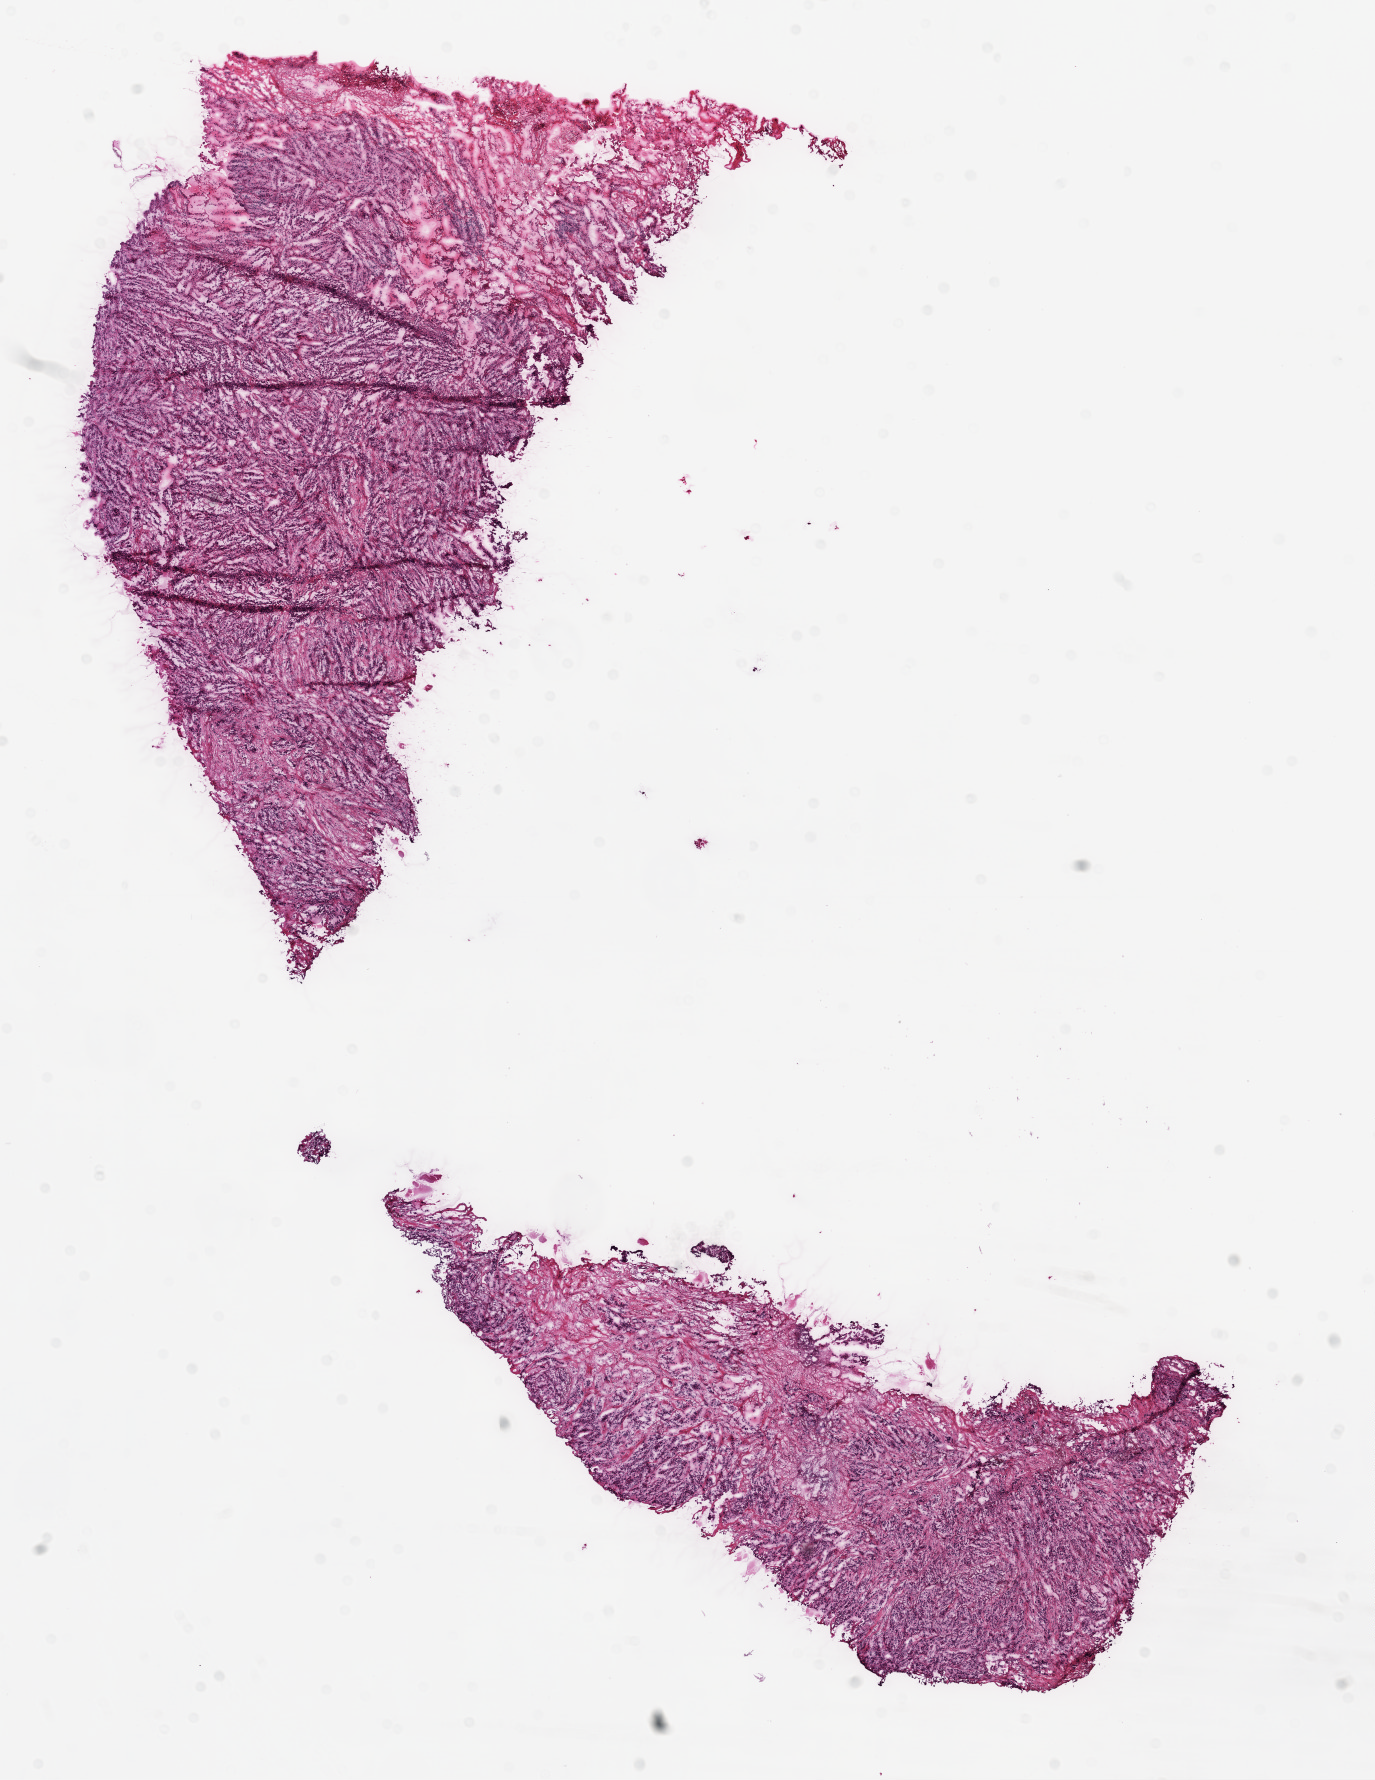
H&E whole-slide image — a low-resolution overview of the entire scanned area, about 11.0 x 14.3 mm. Frozen section. Lung, primary tumour sample. Male patient; age at initial diagnosis 58 years. Composition of this section per pathologist review: tumour cells 45%, tumour nuclei 90%, normal cells 2%, stromal cells 52%, necrosis 1%.
Laterality: right. Histologic diagnosis: Adenocarcinoma, NOS (lower lobe, lung). TNM: T1a N0 M0. AJCC pathologic stage: IA.